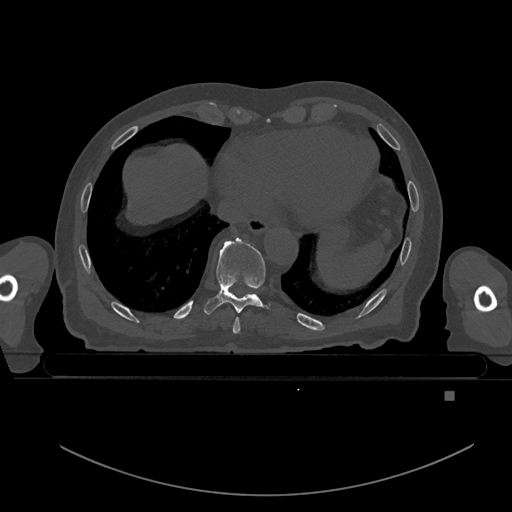
CT including the spine, one axial slice. Slice 146 of 969 in the series (ordered by position). Bone window (W 1800 / L 400 HU). 0.5 mm slice thickness. 512 × 512 image matrix, field of view 456 × 456 mm. Male patient, age 82 years. From the clinical record (not read from this slice): primary cancer: prostate.
Outlined on this slice (semi-automatic segmentation, software-assisted and operator-edited):
- T8 vertebra: box from (x=233, y=317) to (x=240, y=334) px
- T9 vertebra: (x=204, y=238)–(x=271, y=315)